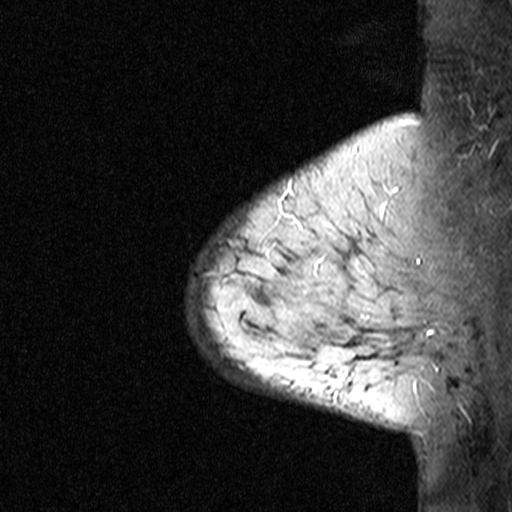
Breast MRI (dynamic contrast-enhanced), one sagittal slice. Slice 36 of 44 in the series (ordered by position). Dynamic contrast-enhanced study with each time point stored as its own series, time point 3 of 4 at this slice position (ordered by acquisition time). 1.5 T. TE 4.5 ms, TR 11 ms. 3 mm slice thickness. 512 × 512 image matrix, field of view 200 × 200 mm. Patient: female, 65 years. From the clinical record (not read from this slice): setting: breast cancer imaged before/during neoadjuvant chemotherapy; receptor status: HER2-positive.
Structures marked on this image (semi-automatically segmented with operator editing):
- analysis volume of interest (the breast-tissue region the enhancement analysis was run in; not a lesion): box from (x=186, y=190) to (x=353, y=361) px
- tumour enhancement mask (voxels above the 90 % enhancement threshold inside the analysis volume of interest): (x=205, y=272)–(x=213, y=276)